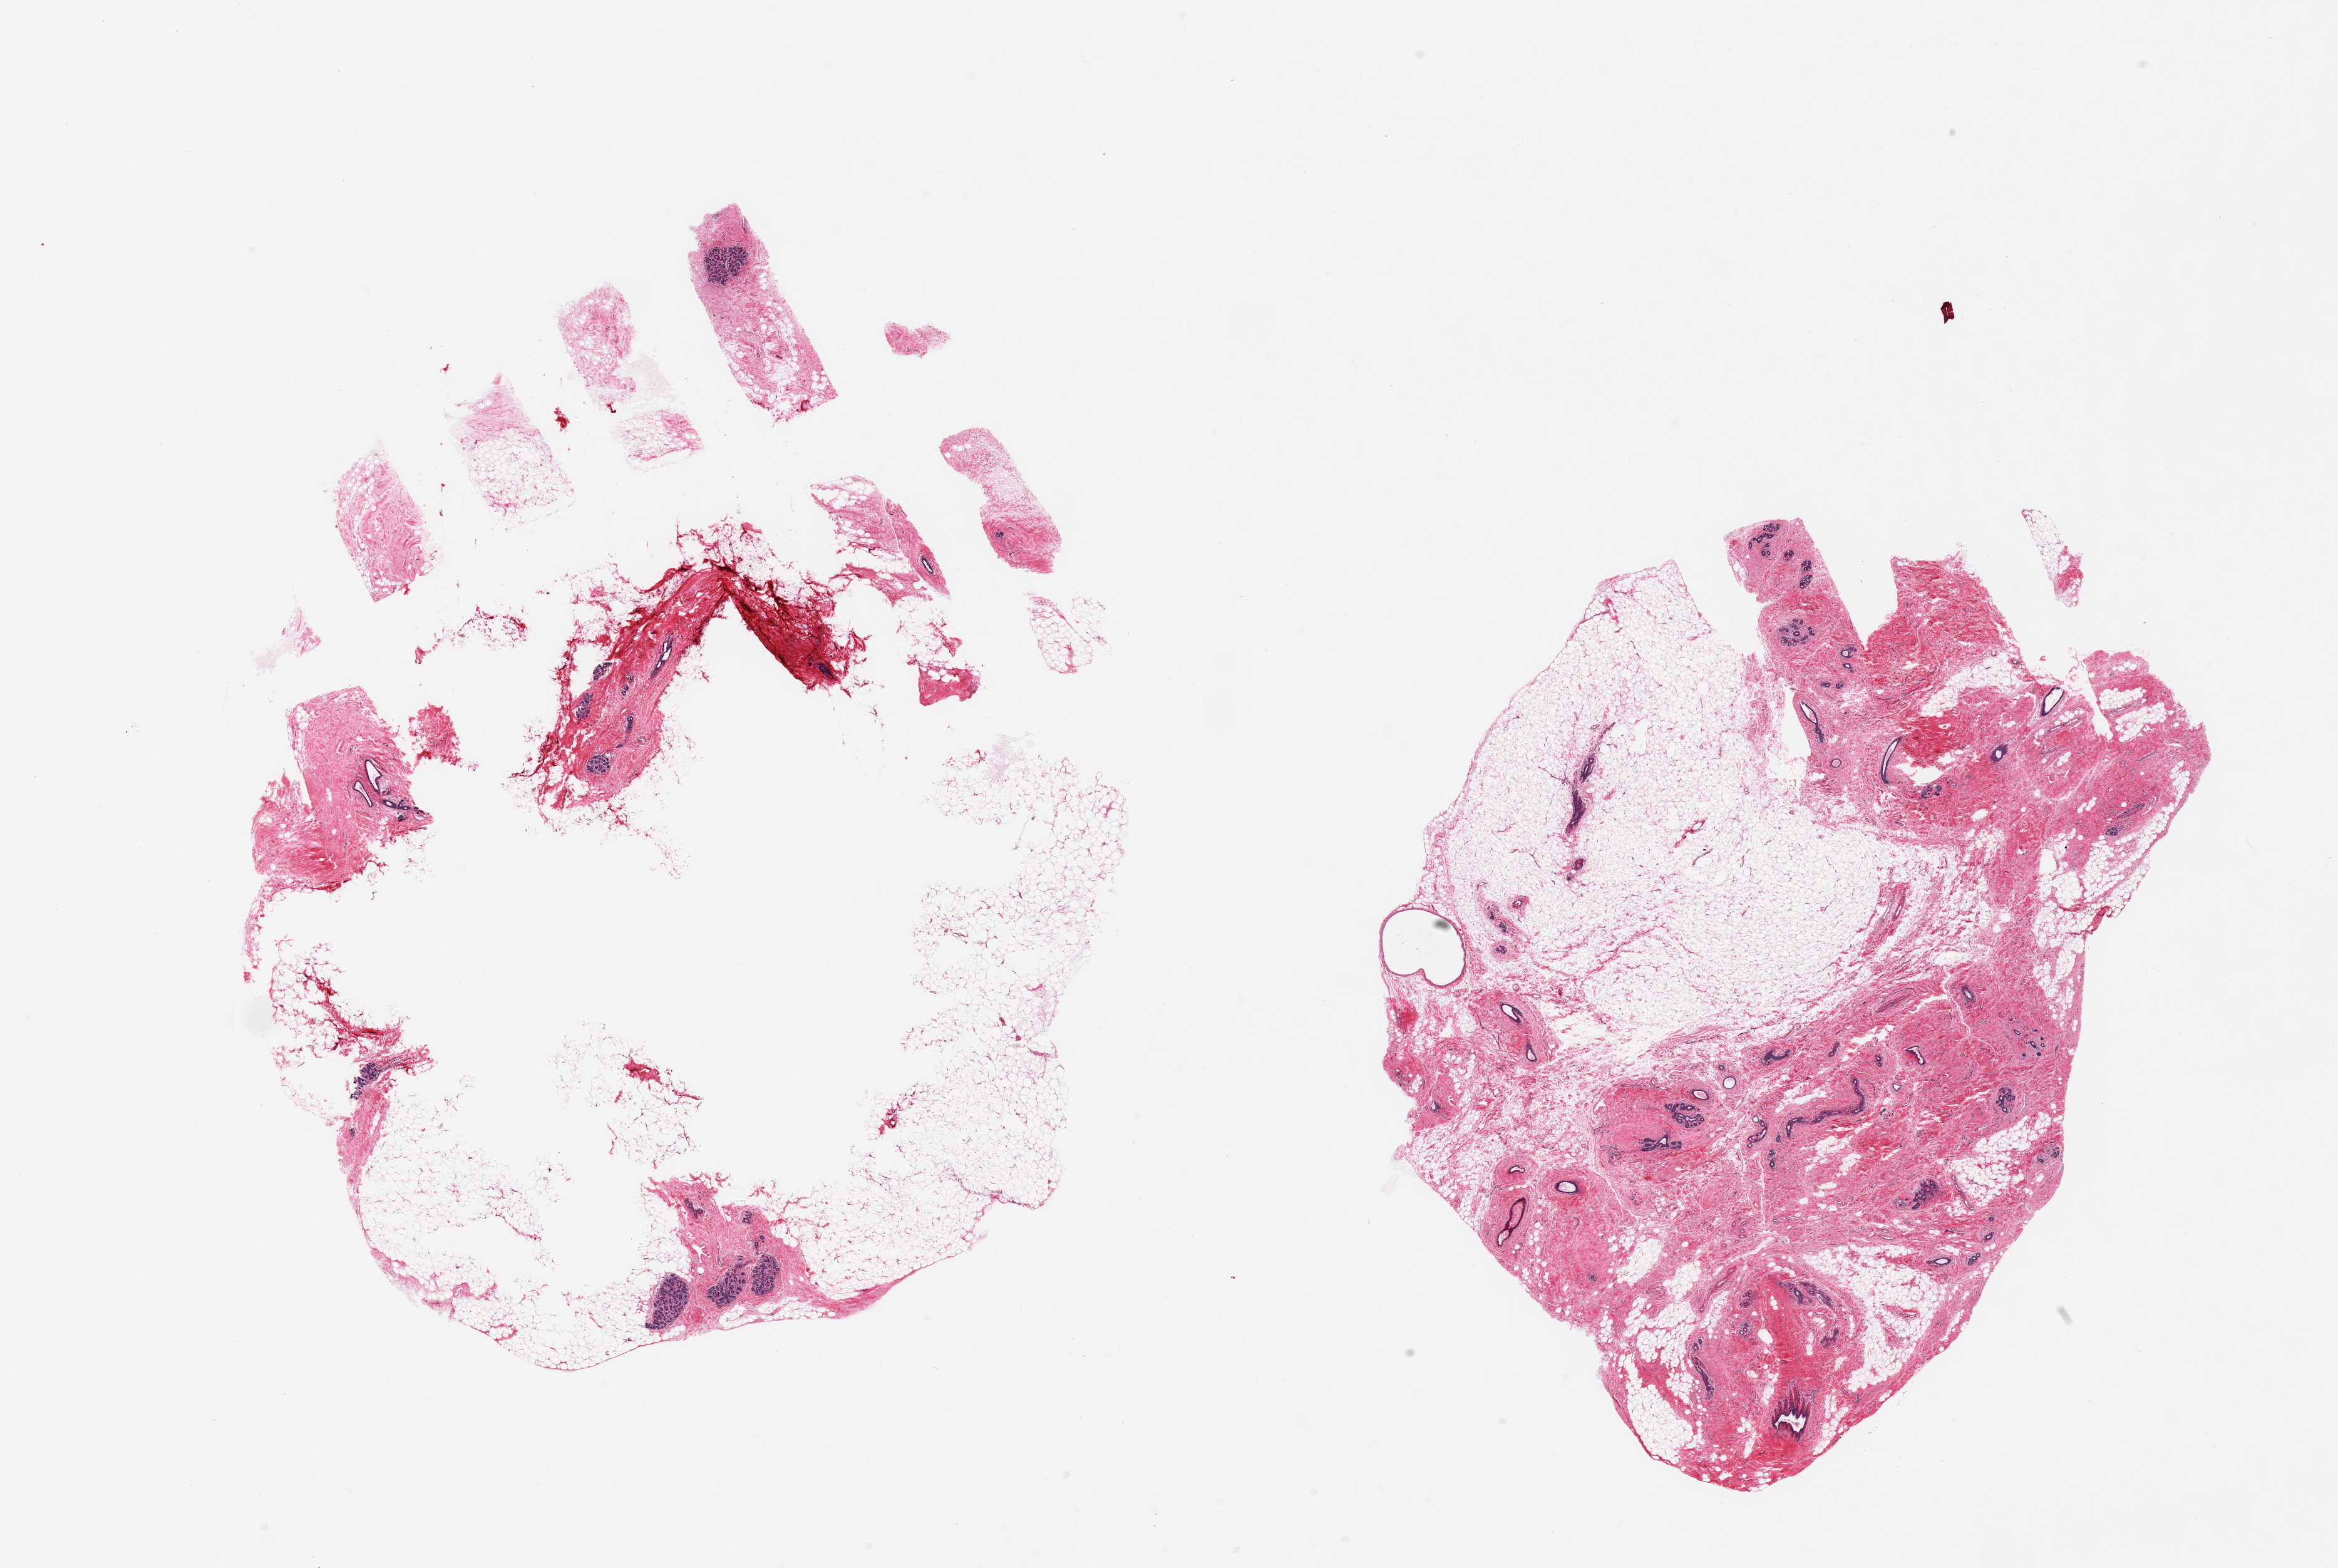
H&E whole-slide image — whole scanned area (about 29.5 x 19.8 mm) shown as a low-resolution overview. PAXgene-fixed paraffin-embedded (PFPE) section. Sampled site (target tissue): breast. Tissue donor sample. Donor sex: female.
Pathologist's review note for this sample: 2 pieces, 1 fragmented; ducts and lobules present.